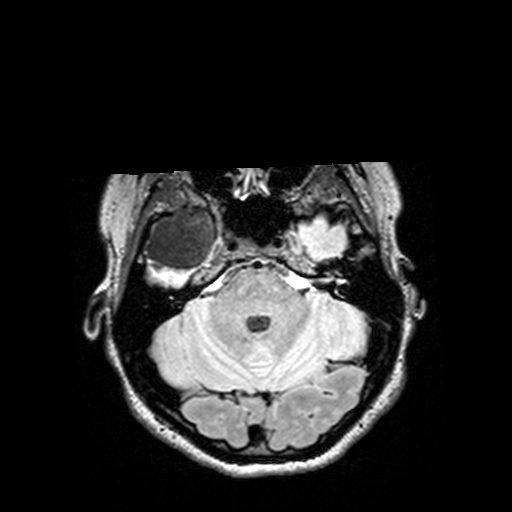
Brain MRI from a brain-tumour surgery series, one axial slice. Slice 106 of 144 in the series (ordered by position). T2 FLAIR. 1 mm slice thickness. 512 × 512 image matrix, field of view 250 × 250 mm. From the clinical record (not read from this slice): histopathology: Astrocytoma; WHO grade: 3; IDH mutation: yes.
Structures marked on this image (manually delineated by an expert):
- tumour: bounding box [x1, y1, x2, y2] px = [126, 209, 232, 274]